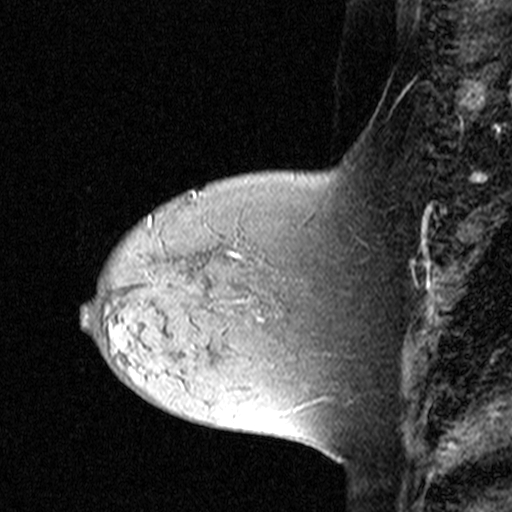
Breast MRI (dynamic contrast-enhanced), one sagittal slice. Slice 12 of 44 in the series (ordered by position). Dynamic contrast-enhanced study with each time point stored as its own series, time point 2 of 3 at this slice position (early post-contrast, ordered by acquisition time). 1.5 T. TE 4.5 ms, TR 11 ms. 3 mm slice thickness. 512 × 512 image matrix, field of view 200 × 200 mm. Patient: female, 44 years. From the clinical record (not read from this slice): setting: breast cancer imaged before/during neoadjuvant chemotherapy; receptor status: triple-negative.
Structures marked on this image (semi-automatic segmentation, software-assisted and operator-edited):
- analysis volume of interest (the breast-tissue region the enhancement analysis was run in; not a lesion): bounding box [x1, y1, x2, y2] px = [132, 212, 309, 331]
- tumour enhancement mask (voxels above the 90 % enhancement threshold inside the analysis volume of interest): [149, 215, 150, 223]